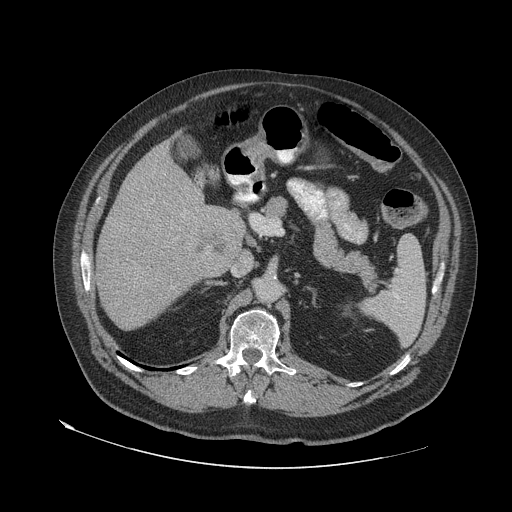
Contrast-enhanced abdominal CT (liver protocol), one axial slice; slice 30 of 79 in the series (ordered by position); reconstruction kernel STANDARD; soft-tissue window (W 400 / L 40 HU); 512 × 512 image matrix, field of view 480 × 480 mm. From the clinical record (not read from this slice): diagnosis: hepatocellular carcinoma (patient treated with transarterial chemoembolisation; whether this scan precedes or follows treatment is not stated here); TNM stage (as recorded): Stage-IVA; Child-Pugh class: A.
Annotated regions visible in this slice (semi-automatic segmentation, software-assisted and operator-edited):
- liver parenchyma outside the tumour (the mass and vessels are separate outlines, so this box may not span the whole liver): bounding box [x1, y1, x2, y2] px = [96, 142, 244, 328]